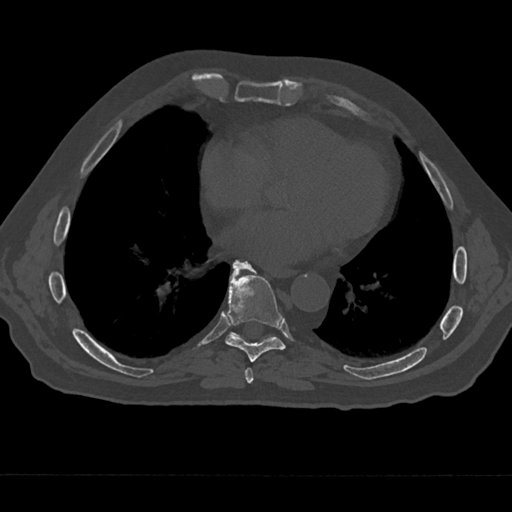
CT including the spine, one axial slice; position 307 of 797 along the scan axis; bone window (W 1800 / L 400 HU); 0.5 mm slice thickness; 512 × 512 image matrix. Patient: male, 75 years. Case-level facts recorded for this patient, not image findings: primary cancer: renal; vertebrae with lytic lesions (as recorded): T4.
Outlined on this slice (semi-automatic segmentation, software-assisted and operator-edited):
- T7 vertebra: bounding box [x1, y1, x2, y2] px = [238, 368, 255, 384]
- T8 vertebra: [225, 260, 286, 362]
- T9 vertebra: [231, 262, 257, 334]